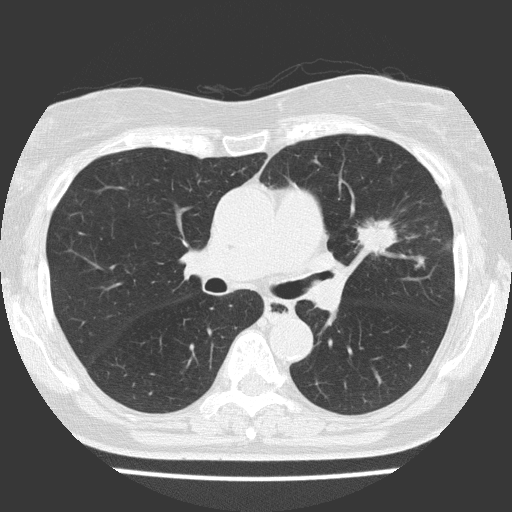
Low-dose screening chest CT, axial slice, baseline annual screen, lung window (W 1500 / L -600 HU), 2 mm slice thickness, 512 × 512 image matrix. Female participant, aged 70 years at enrolment. Current smoker at enrolment.
- Expert reader's lesion annotation, bounding box [x1, y1, x2, y2] px = [327, 193, 432, 283].
- The screening reader recorded 2 non-calcified nodules or masses ≥4 mm on this exam; which of them this box marks is not recorded.
- Official screen result: positive, change unspecified: nodule(s) >= 4 mm or enlarging nodule(s), mass(es), or other non-specific abnormalities suspicious for lung cancer.
- Participant outcome: lung cancer diagnosed 25 days after this screen — adenocarcinoma, NOS, left upper lobe, poorly differentiated (G3), stage IV (AJCC 6th edition), 30 mm at pathology.